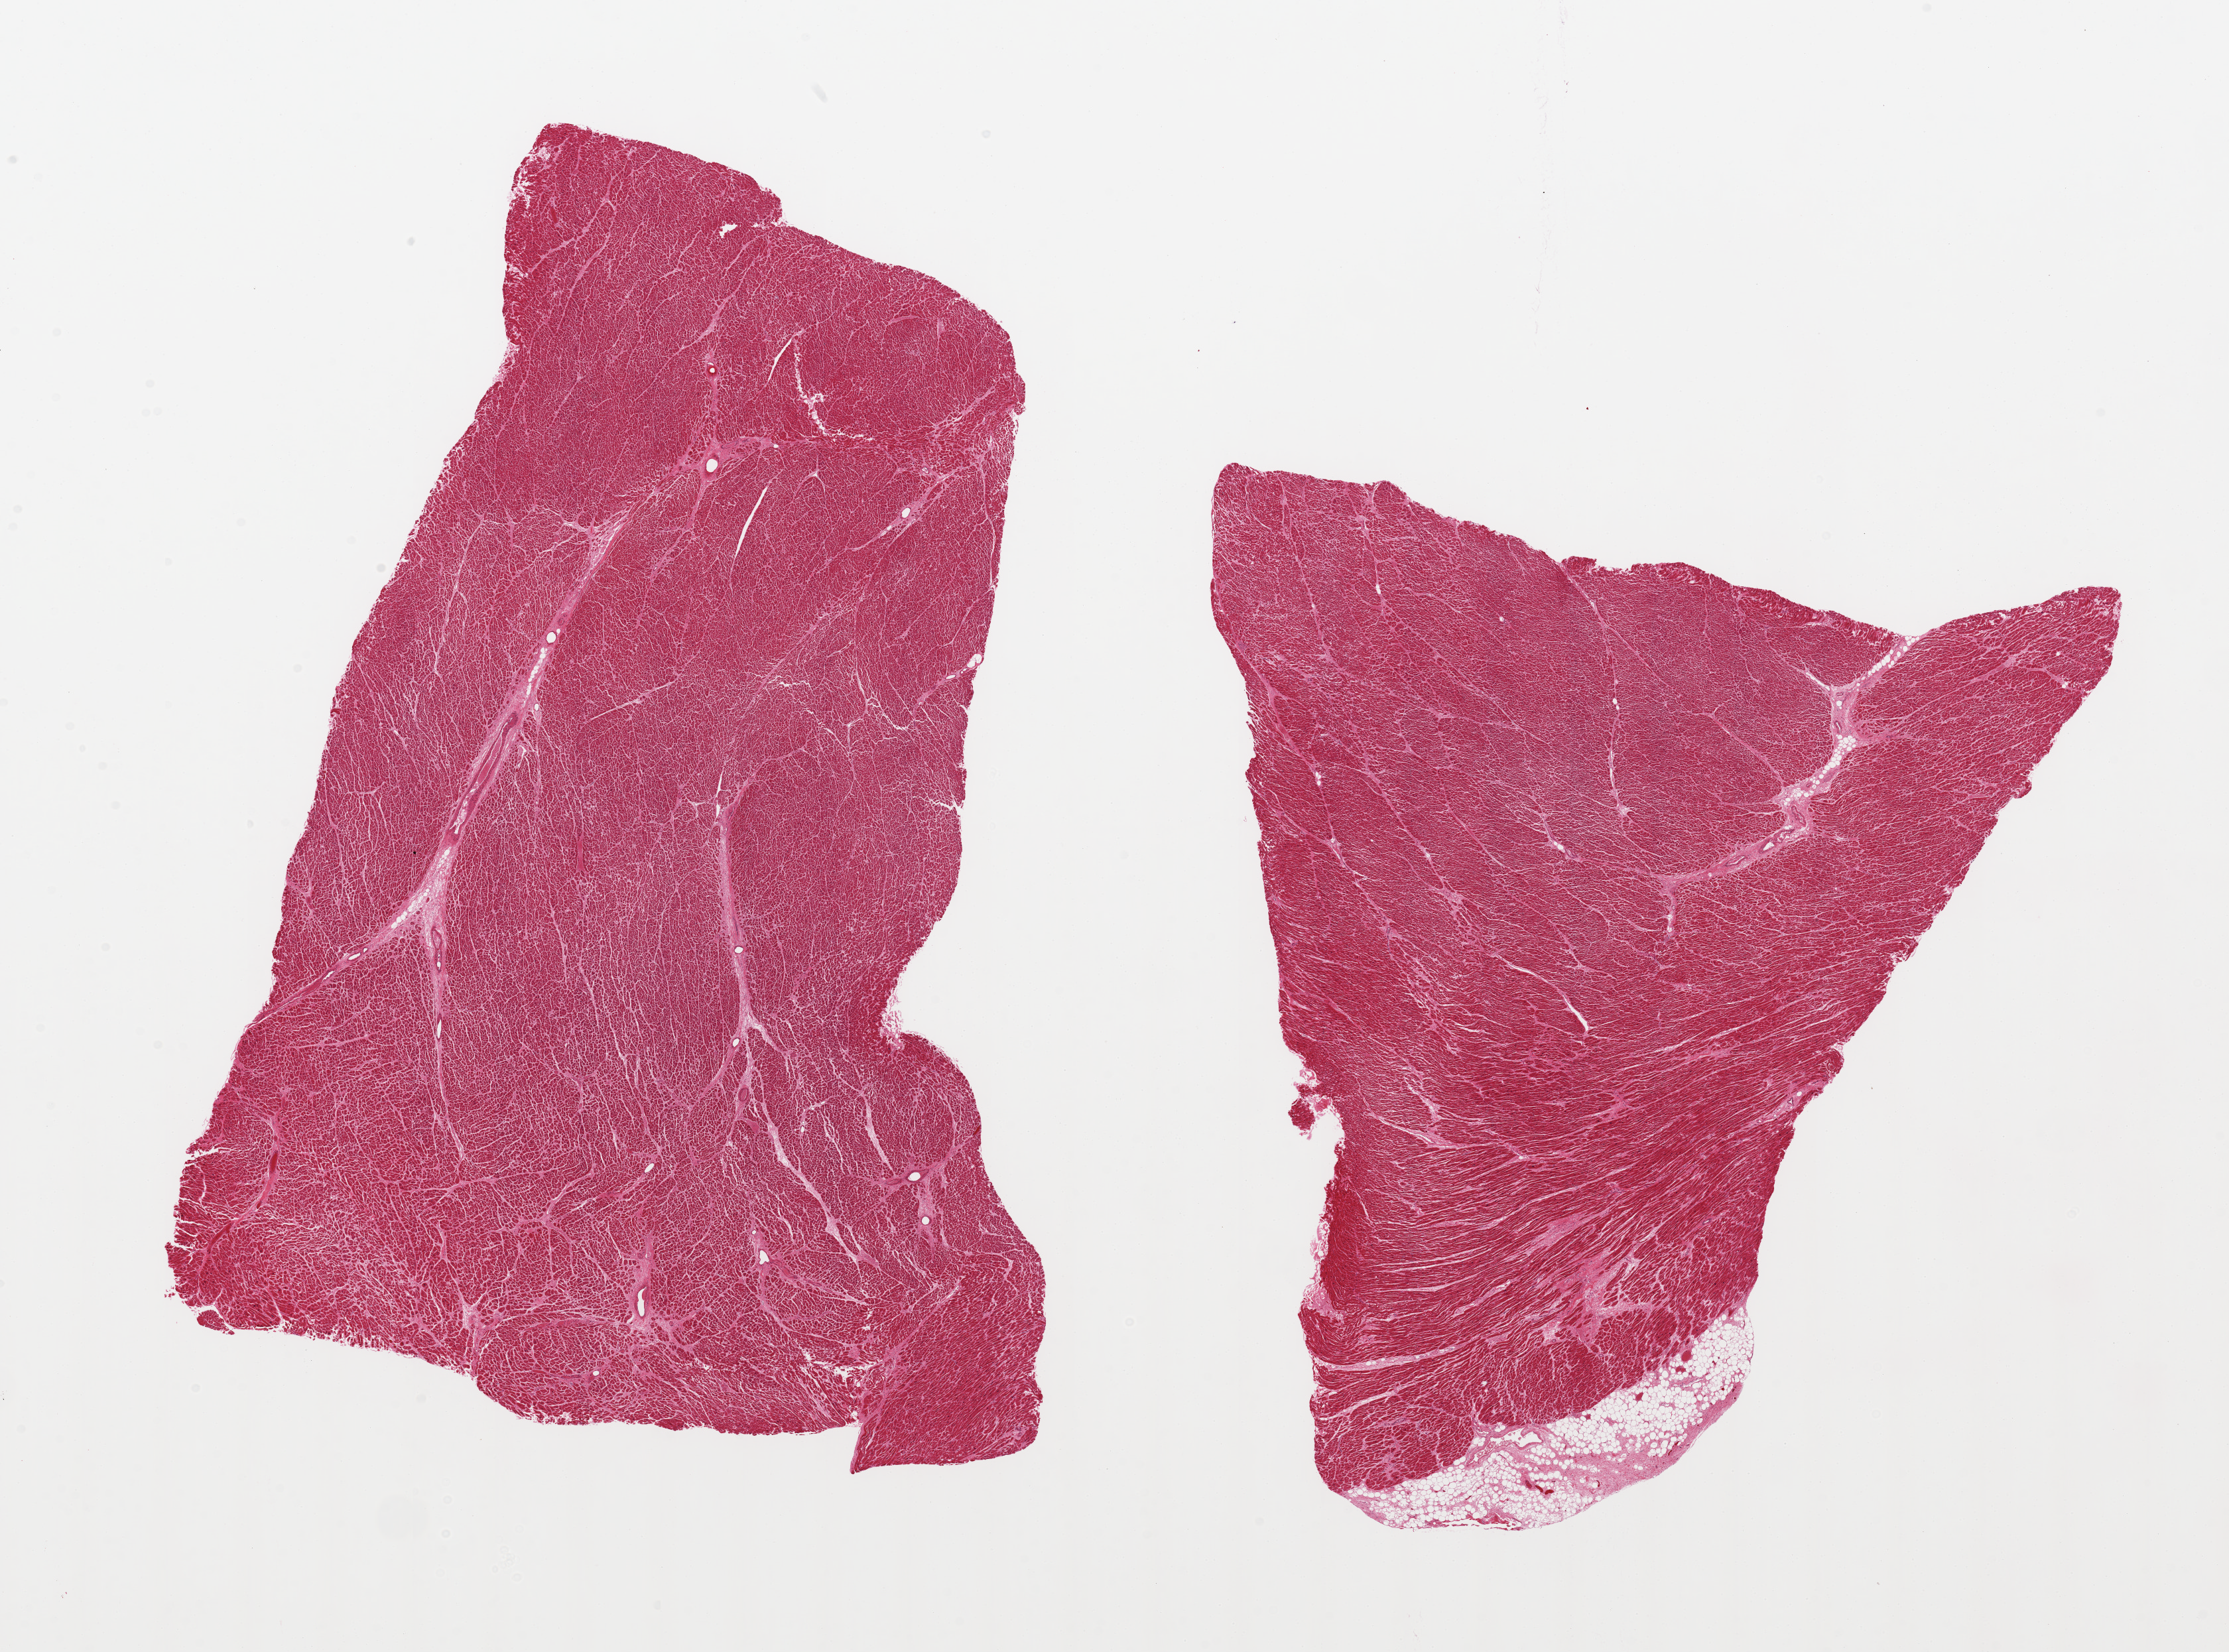
Hematoxylin and eosin (H&E) whole-slide image — low-resolution overview of the scanned area, about 26.6 x 19.7 mm (acquisition: 20x scan), PAXgene-fixed, paraffin-embedded tissue, sampled site (target tissue): heart, tissue donor sample. Donor: male.
* review note (as recorded): 2 pieces